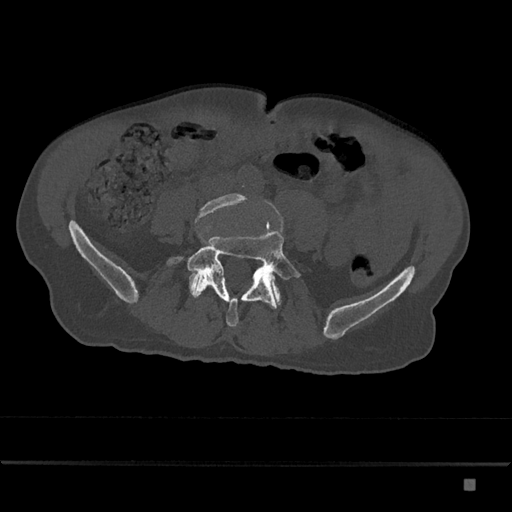
CT including the spine, one axial slice; slice 287 of 797 in the series (ordered by position); 120 kVp; bone window (W 1800 / L 400 HU); 0.5 mm slice thickness; 512 × 512 image matrix, field of view 390 × 390 mm. Patient: male, 72 years. Case-level facts recorded for this patient, not image findings: primary cancer: prostate.
Annotated regions visible in this slice (semi-automatic segmentation, software-assisted and operator-edited):
- L4 vertebra: bounding box (x1, y1, x2, y2) in pixels: (194, 193, 249, 224)
- L5 vertebra: (167, 231, 302, 327)